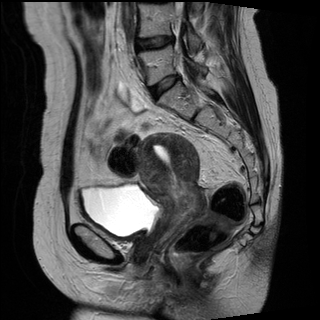
Pelvic MRI for cervical cancer, one sagittal slice. Slice 12 of 27 in the series (ordered by position). T2-weighted. 1.5 T. TE 89 ms, TR 2740 ms. 4 mm slice thickness. 320 × 320 image matrix, field of view 260 × 260 mm. Female patient, age 42 years.
Annotated regions visible in this slice (expert manual segmentation):
- uterus and cervix: bounding box (x1, y1, x2, y2) in pixels: (138, 131, 202, 243)